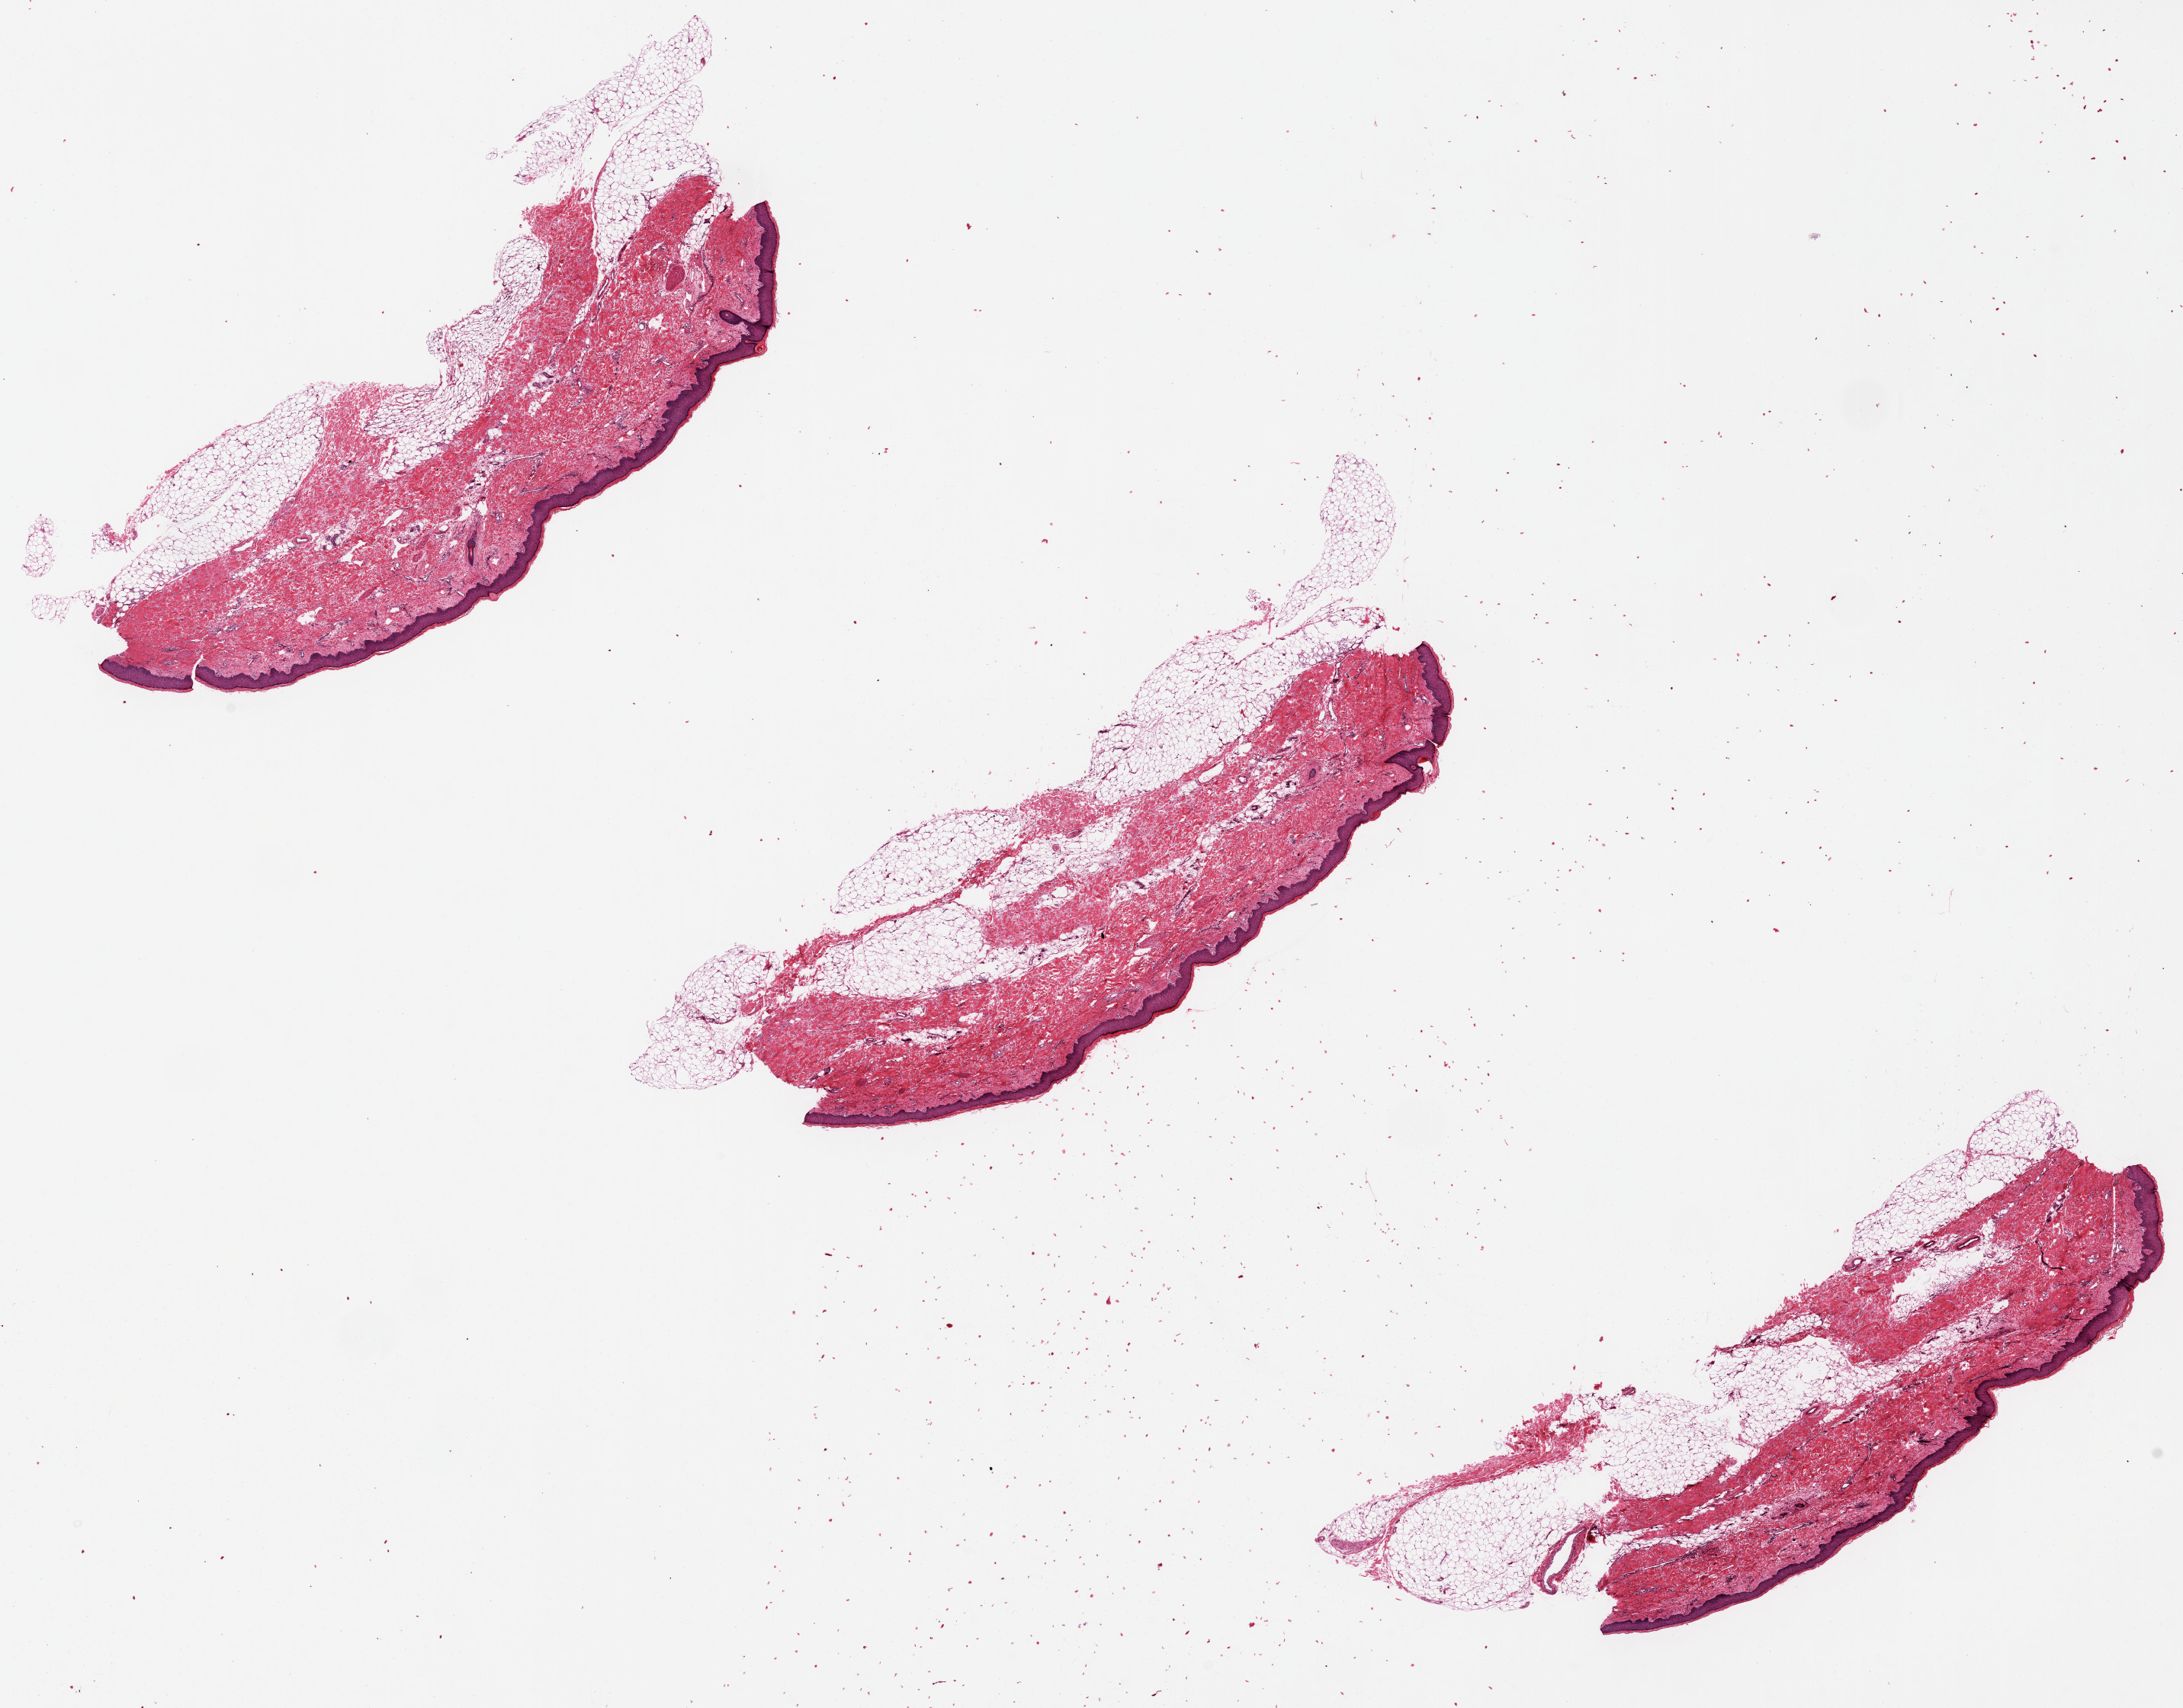
Whole-slide image, hematoxylin and eosin (H&E) stain, a low-resolution overview of the entire scanned area, about 22.6 x 17.7 mm; PAXgene-fixed, paraffin-embedded tissue; target tissue: skin of lower leg; donor tissue sample. Donor: female.
* review note (as recorded): Epithelium is 5-8% of specimen thickness